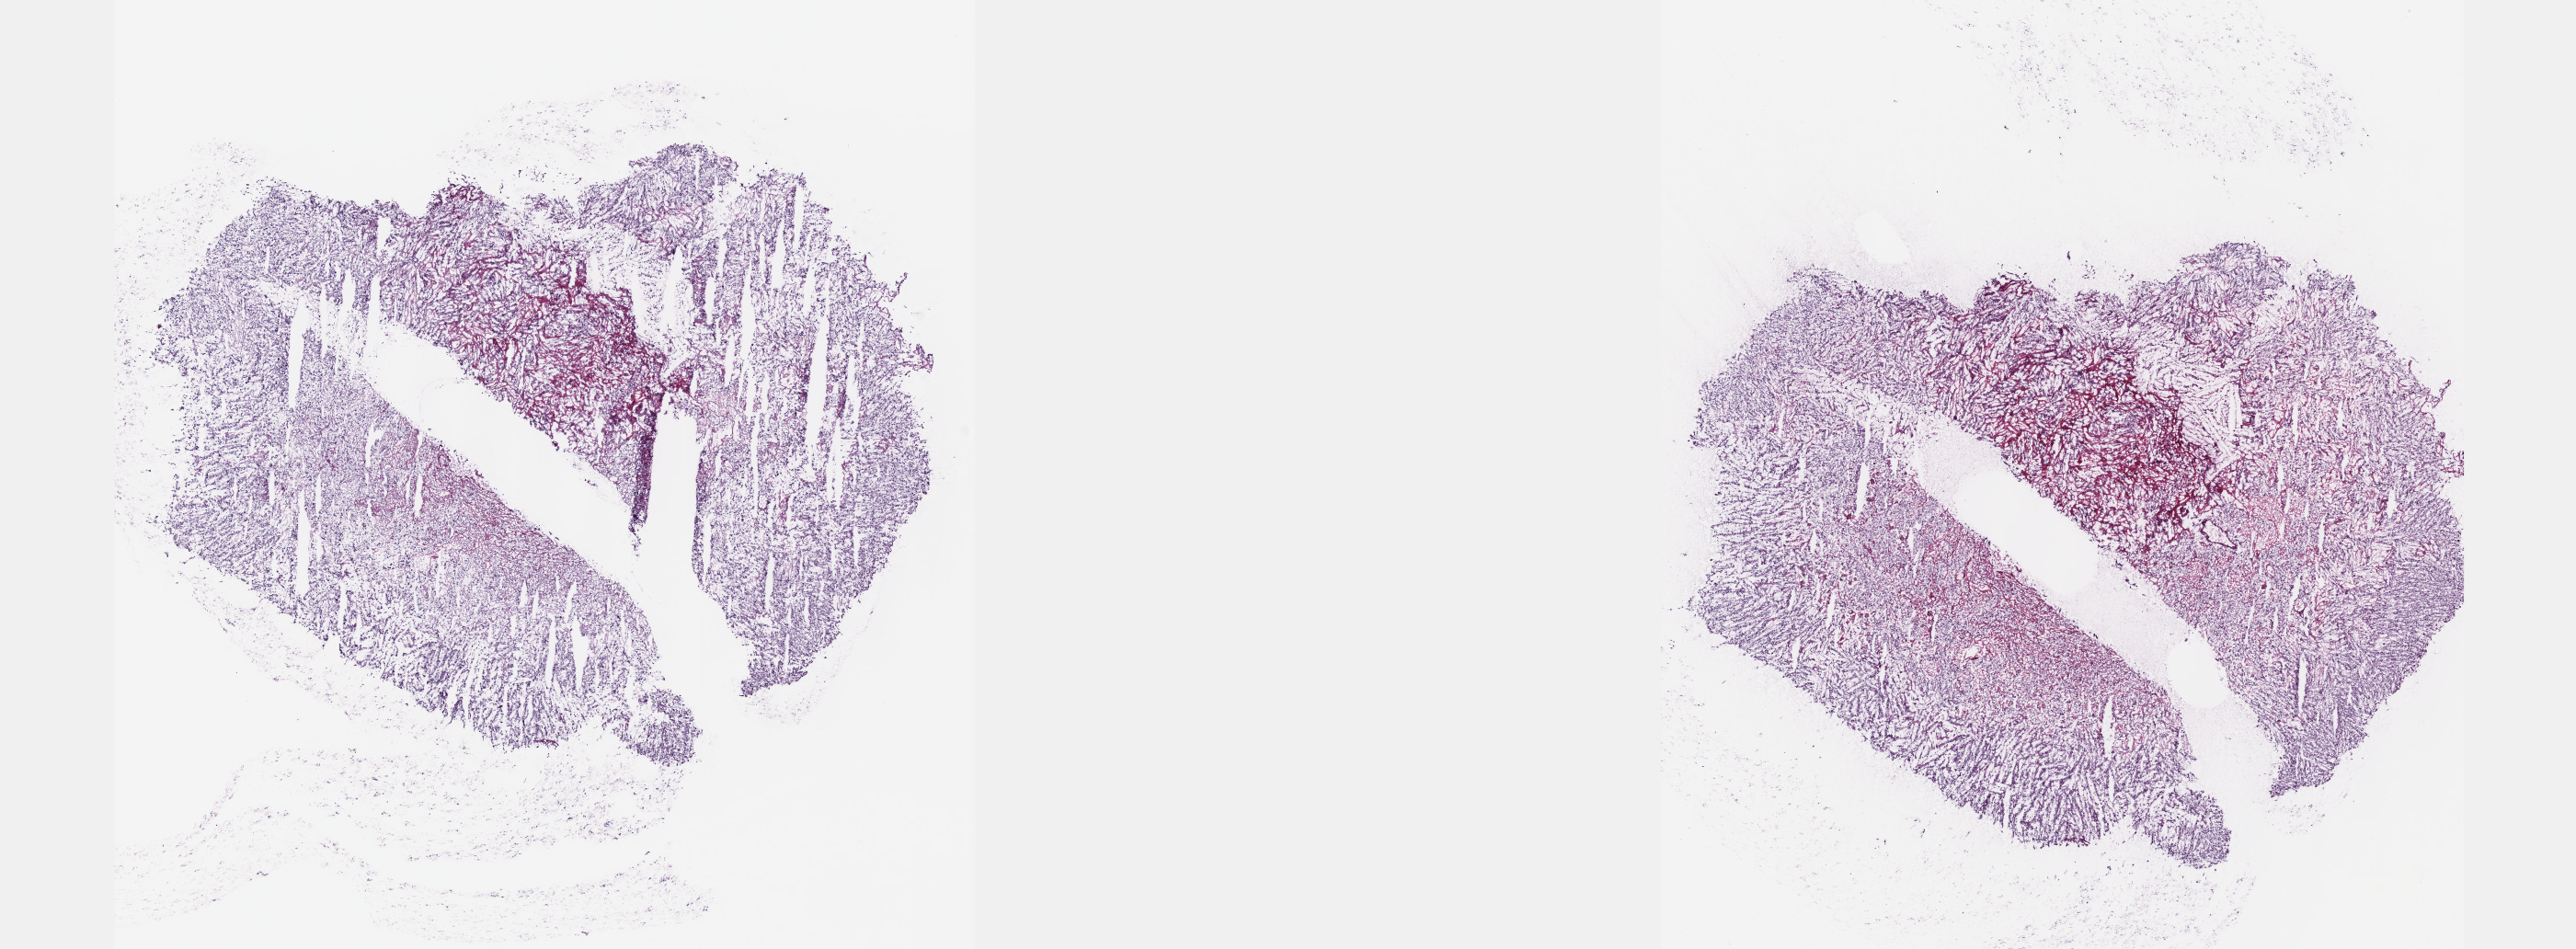
Digitized H&E-stained tissue section (whole slide), shown as a low-resolution overview of the whole scanned area (about 22.6 x 8.3 mm, from a 40x scan); frozen section; adrenal gland, primary tumour sample. Male, age 74 years at initial diagnosis.
Pathologic diagnosis: Pheochromocytoma, malignant.